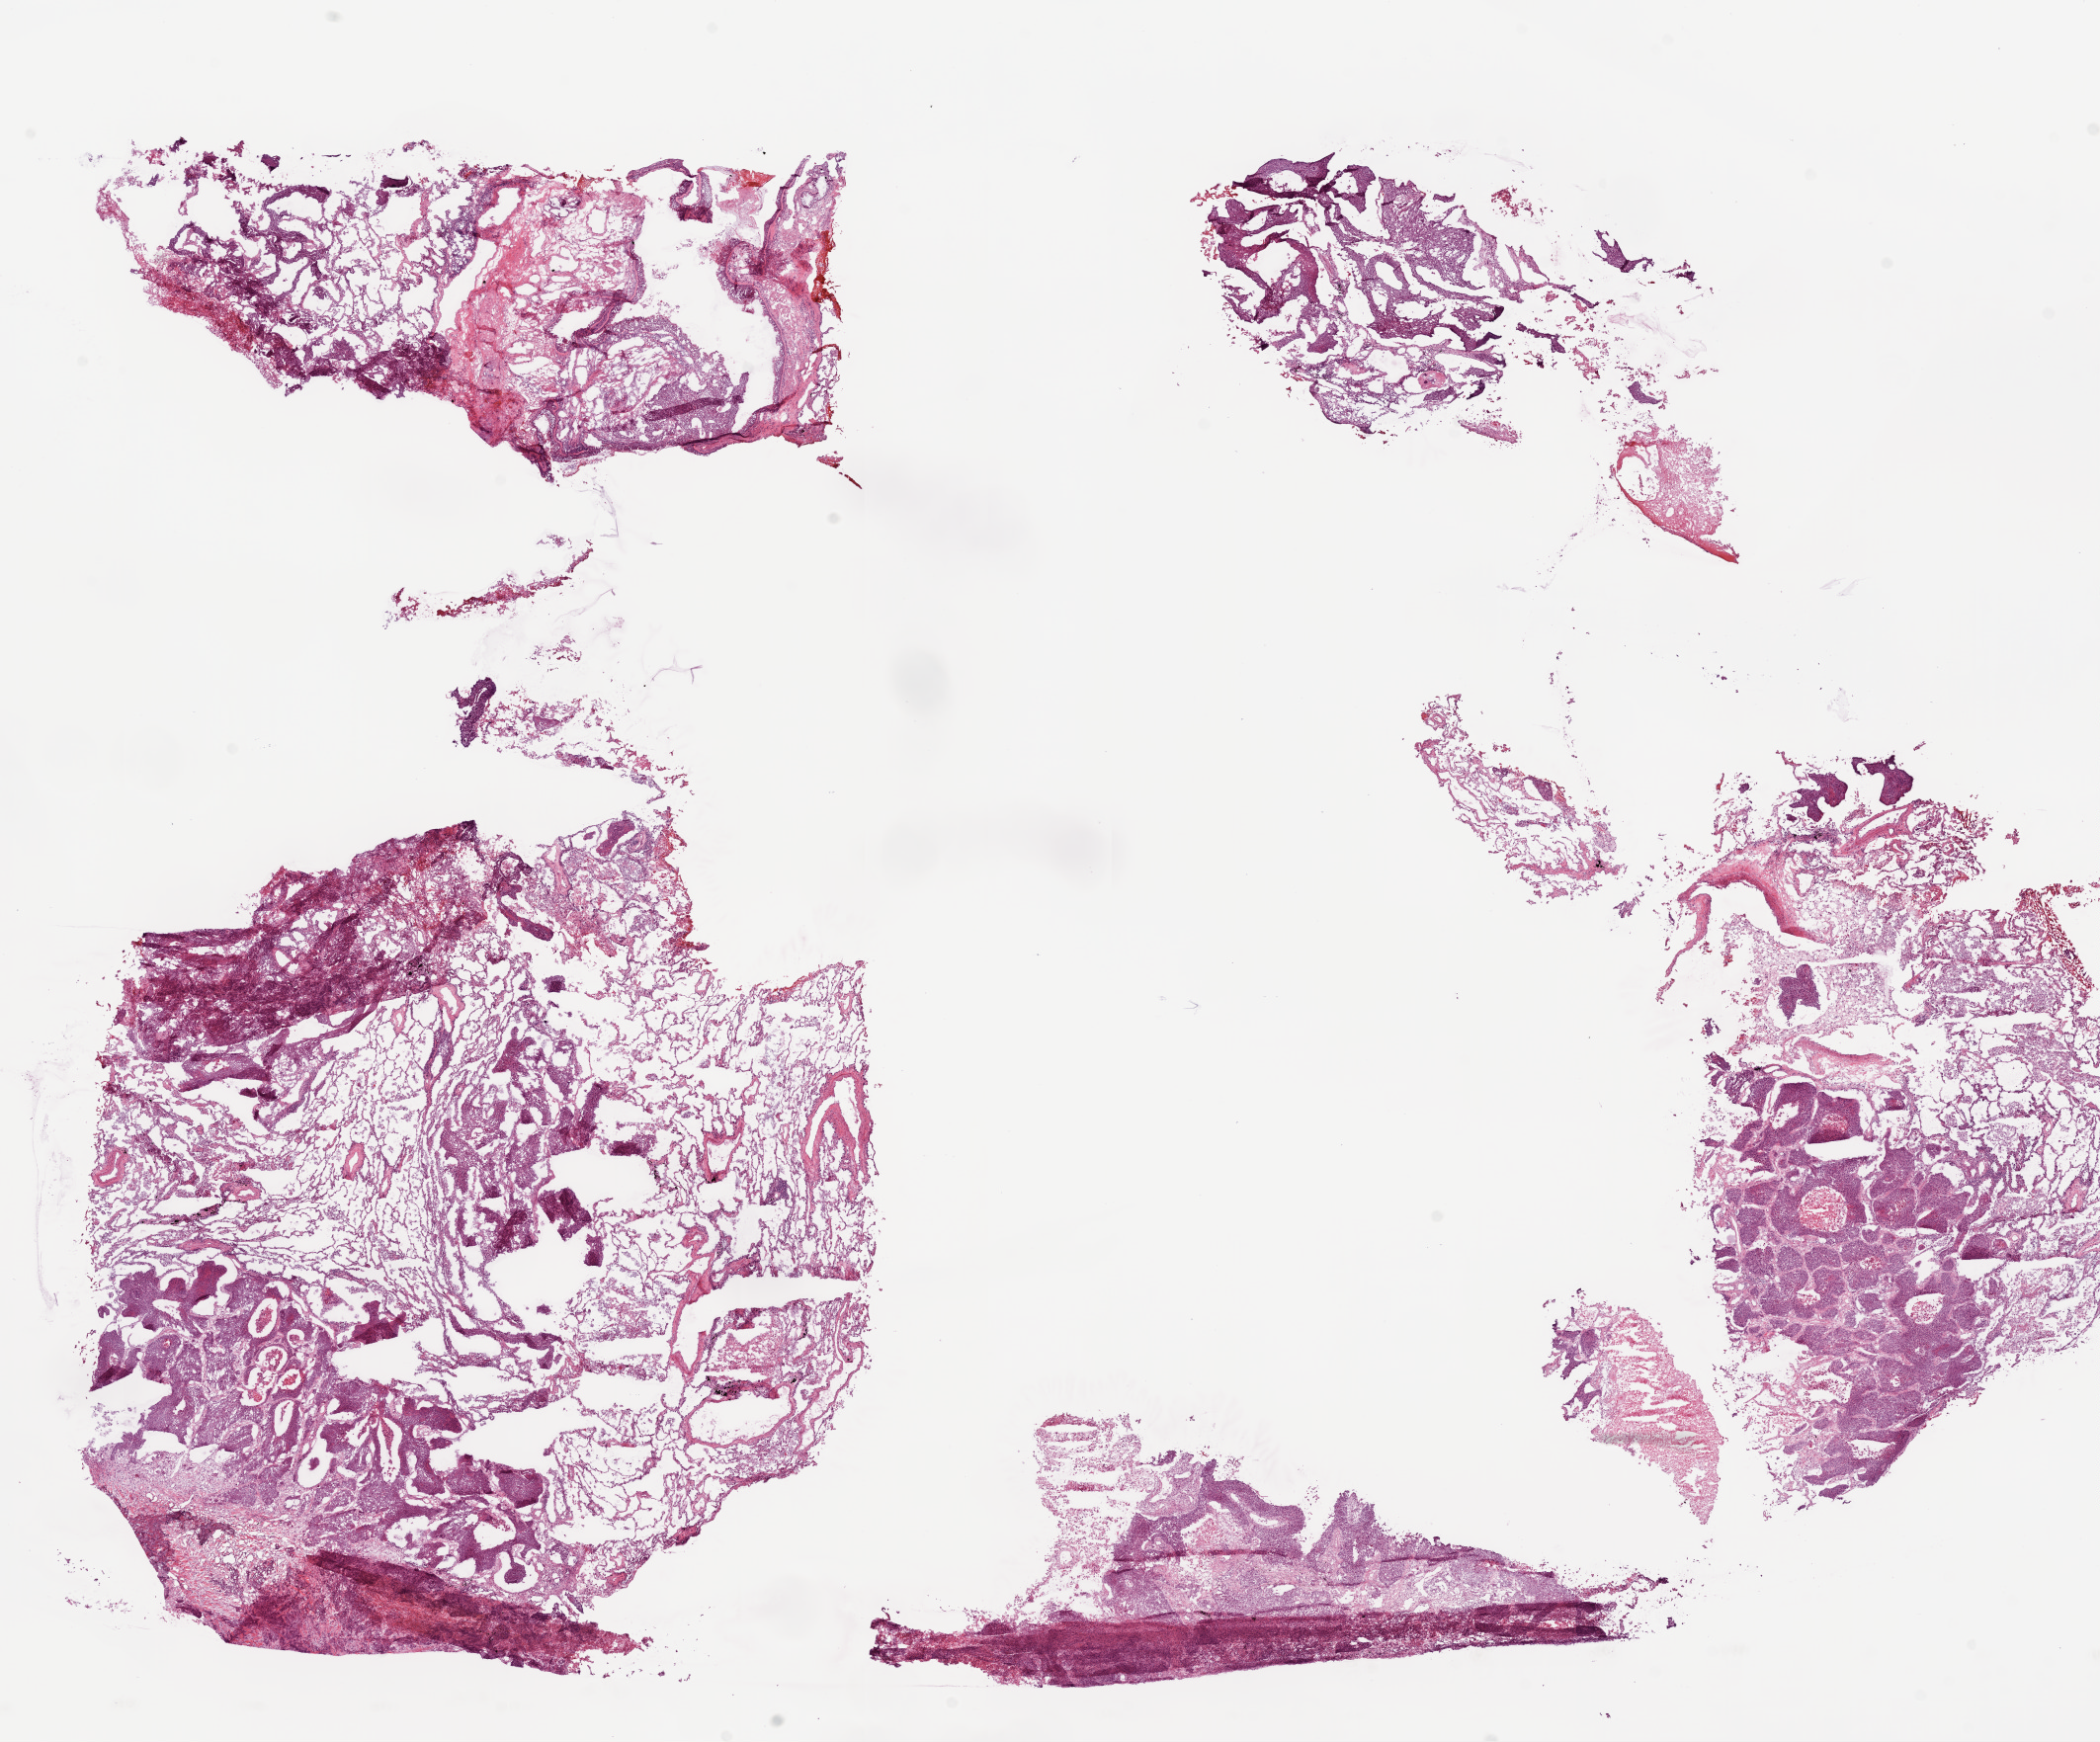
Digitized Hematoxylin and eosin (H&E) stained tissue section (whole slide), a low-resolution overview of the entire scanned area, about 17.1 x 14.1 mm (from a 20x scan). Frozen section from the bottom of the tissue portion. Lung, primary tumour sample. Male patient; age at initial diagnosis 73 years. Composition of this section per pathologist review: tumour cells 50%, tumour nuclei 55%, normal cells 40%, stromal cells 5%, necrosis 5%.
• pathologic diagnosis: Squamous cell carcinoma, NOS (lower lobe, lung)
• AJCC pathologic stage: IB (7th edition)